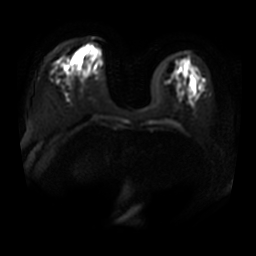
Breast MRI, one axial slice; position 11 of 34 along the scan axis; diffusion-weighted series; image 2 of 4 stored at this slice position (different b-values; order by instance number); 3 T; 5 mm slice thickness; 256 × 256 image matrix, field of view 380 × 380 mm. Female patient.
Annotated regions visible in this slice (manually delineated by an expert):
- tumour on diffusion-weighted imaging: bounding box (x1, y1, x2, y2) in pixels: (79, 48, 87, 54)